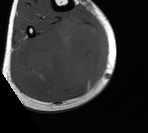
MRI of an extremity soft-tissue mass, one axial slice; slice 67 of 76 in the series (ordered by position); MR volume resampled by the dataset authors to the PET/CT grid (not the native acquisition matrix); 148 × 133 image matrix, field of view 145 × 130 mm. Male patient. Case-level facts recorded for this patient, not image findings: histological type: liposarcoma - round cell; grade: high; site of the primary tumour: right calf.
Structures marked on this image (expert contour drawn on MRI and transferred to this co-registered scan by the dataset authors):
- gross tumour volume (mass): bounding box [x1, y1, x2, y2] px = [17, 19, 103, 93]